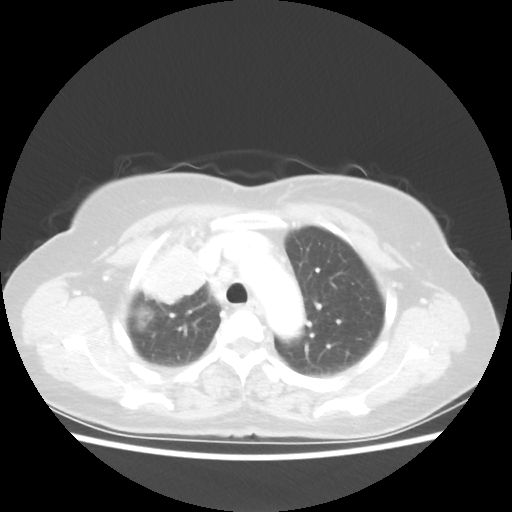
Chest CT, one axial slice. Slice 41 of 55 in the series (ordered by position). Reconstruction kernel STANDARD. Lung window (W 1500 / L -600 HU). 5 mm slice thickness. 512 × 512 image matrix, field of view 337 × 337 mm. Patient: female, 62 years. Case-level facts recorded for this patient, not image findings: clinical TNM (as recorded): T4 N3 M0.
Annotated regions visible in this slice (rectangle marked by the reading radiologist):
- lung tumour (recorded histology: squamous cell carcinoma): bounding box (x1, y1, x2, y2) in pixels: (131, 242, 209, 312)